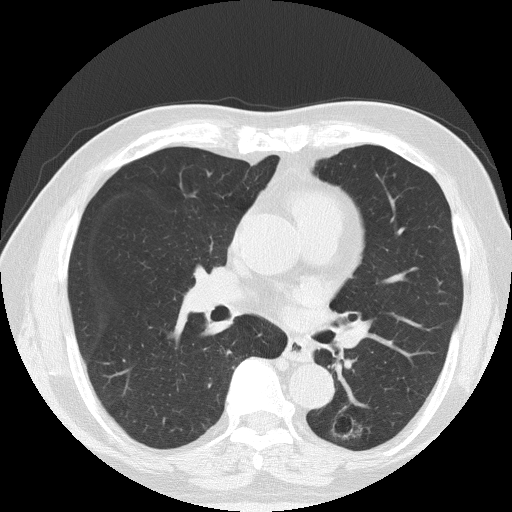
Chest CT (low-dose screening protocol), one axial image, baseline annual screen, lung window (W 1500 / L -600 HU), 2 mm slice thickness, lung (sharp) reconstruction kernel (FC51), slice 77 of 145 in the series, 512 × 512 image matrix, field of view 340 × 340 mm. Male, age 71 years at enrolment. Former smoker at enrolment.
Lesion marked by an expert reader, box from (x=322, y=408) to (x=373, y=451) px. No non-calcified nodule or mass ≥4 mm was recorded by the screening reader at this exam. Participant outcome: lung cancer diagnosed 340 days after this screen — adenocarcinoma, NOS, left lower lobe, poorly differentiated (G3), stage IA (AJCC 6th edition), 28 mm at pathology.